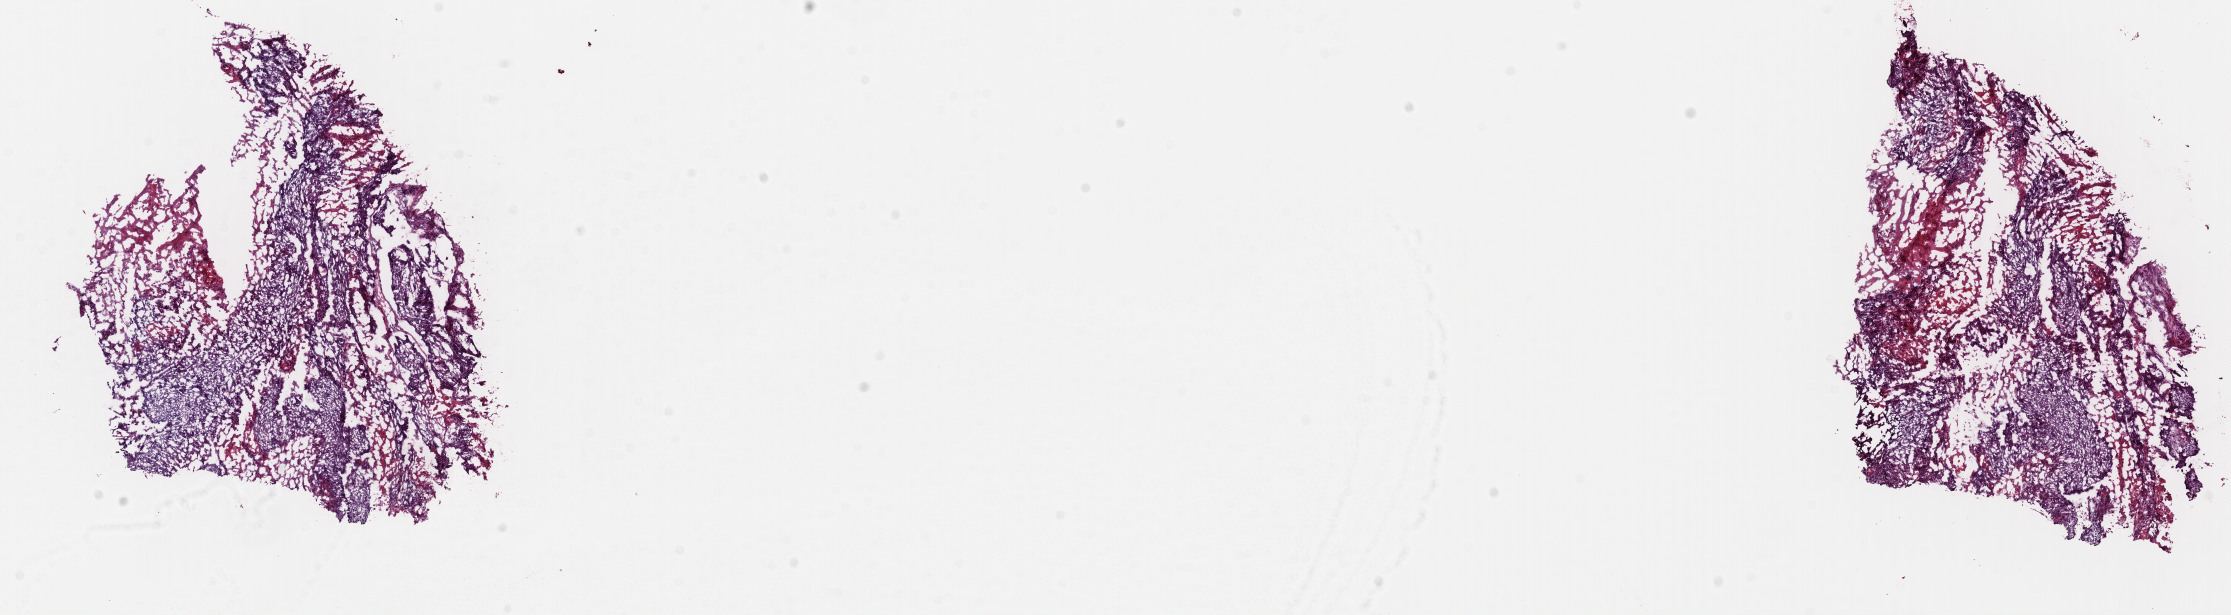
H&E whole-slide image — a low-resolution overview of the entire scanned area, about 17.6 x 4.9 mm (from a 40x scan), frozen section from the top of the tissue portion, primary tumour sample from the cervix. Female, age 81 years at initial diagnosis. Histologic grade: G3 (poorly differentiated). Slide review estimates, as recorded: tumour cells 80%, tumour nuclei 96%, normal cells 0%, stromal cells 5%, necrosis 15%. Inflammatory infiltration, as recorded: lymphocyte infiltration 1%, monocyte infiltration 0%, neutrophil infiltration 0%.
• FIGO stage: IIB
• pathologic diagnosis: Squamous cell carcinoma, keratinizing, NOS (cervix uteri)